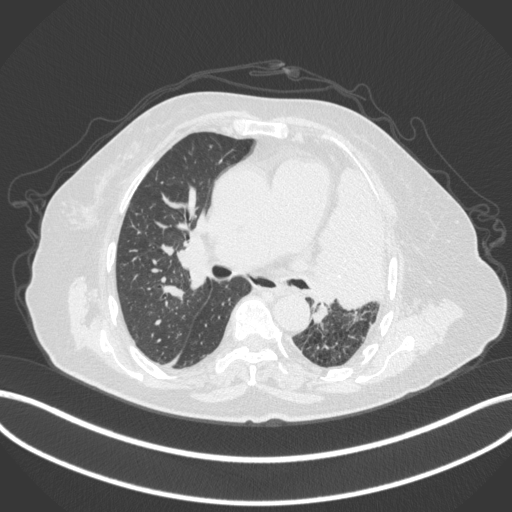
Chest CT, one axial slice. Slice 222 of 399 in the series (ordered by position). Reconstruction kernel B31f. Lung window (W 1500 / L -600 HU). 1 mm slice thickness. 512 × 512 image matrix, field of view 400 × 400 mm. Patient: female, 75 years. Case-level facts recorded for this patient, not image findings: clinical TNM (as recorded): T3 N3 M1.
Outlined on this slice (rectangle marked by the reading radiologist):
- lung tumour (recorded histology: adenocarcinoma): bounding box [x1, y1, x2, y2] px = [305, 157, 389, 312]